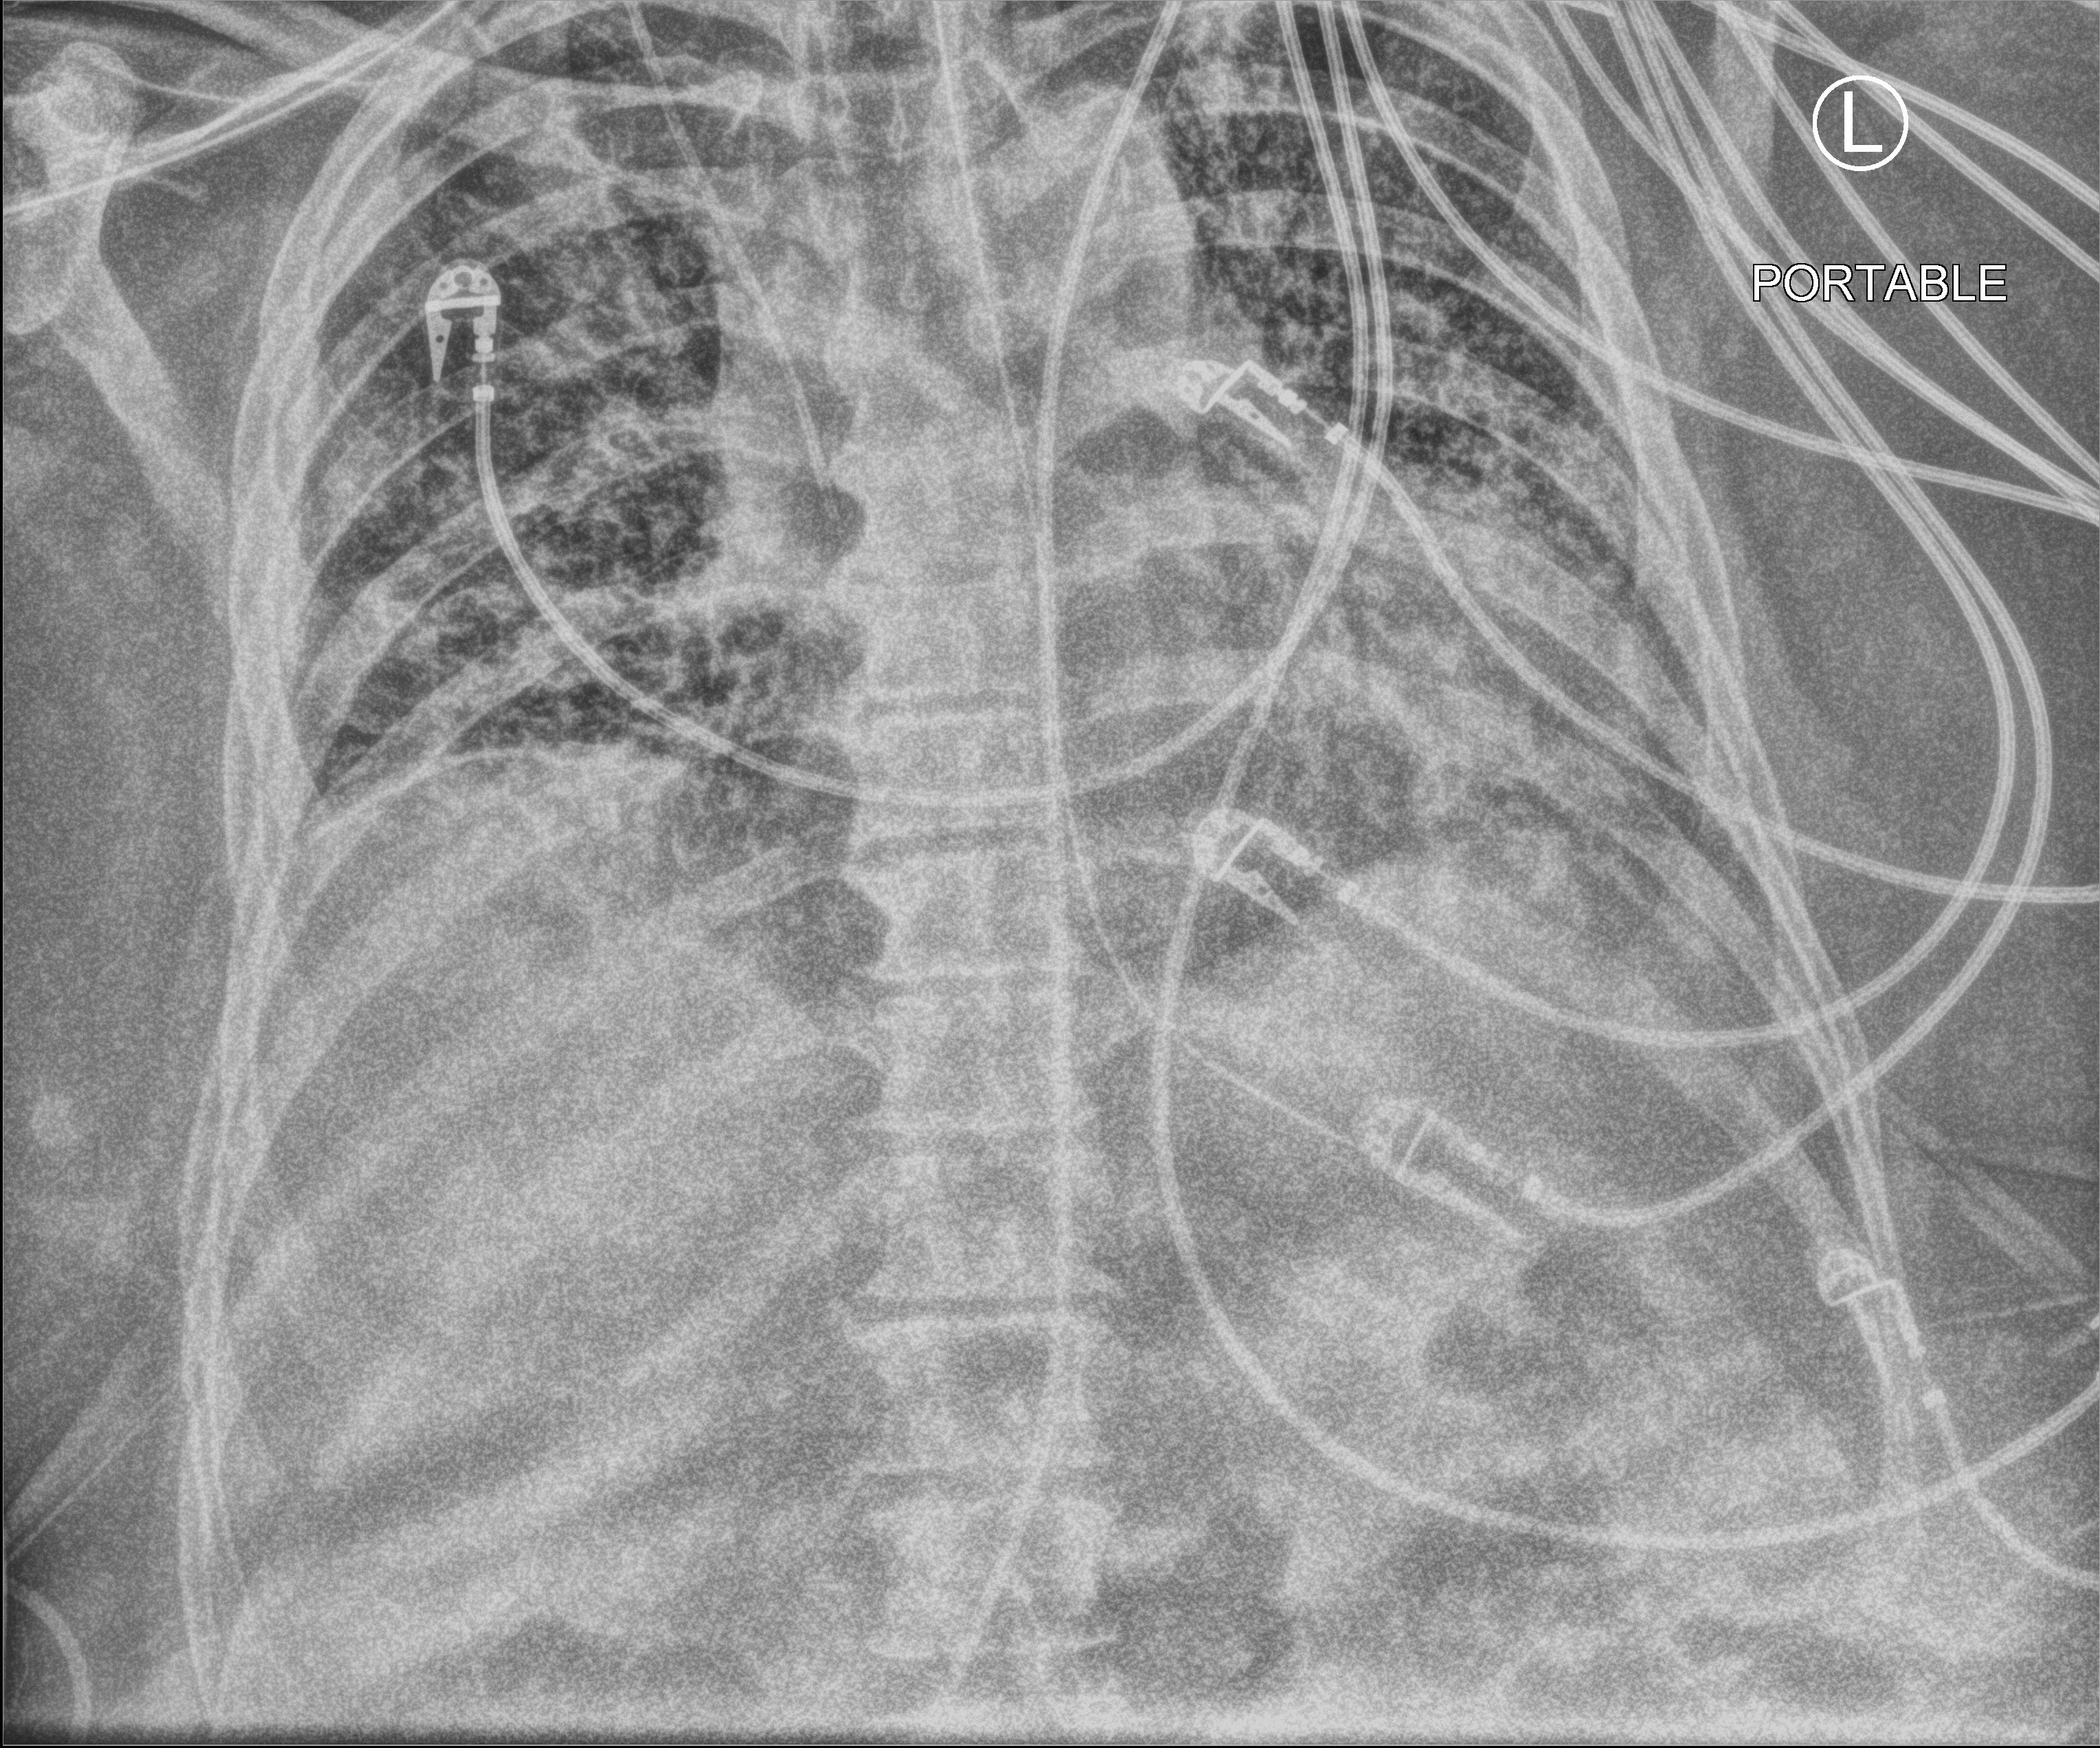
Chest X-ray (portable), anteroposterior (AP) projection. Patient hospitalised with COVID-19; male, aged 60–74 years.
Hospital-stay facts (about this admission, not read from this image; timing relative to this image not recorded): hypertension (admission record): yes; admitted to intensive care during this hospital stay: yes; length of hospital stay: 40 days.